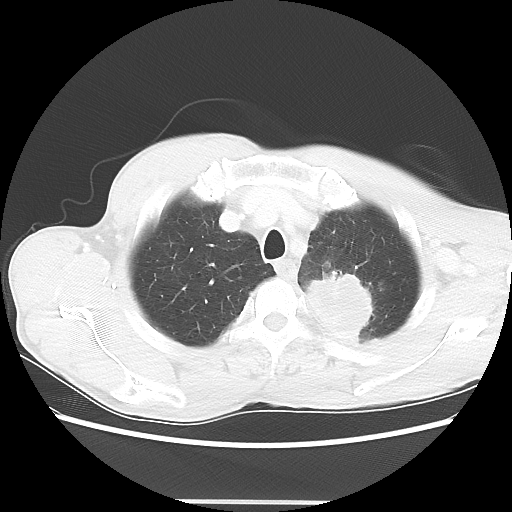
Chest CT, one axial slice. Reconstruction kernel LUNG. 100 kVp. Lung window (W 1500 / L -600 HU). 5 mm slice thickness. 512 × 512 image matrix, field of view 360 × 360 mm. Male patient, age 61 years. From the clinical record (not read from this slice): clinical TNM (as recorded): T3 N1 M1.
Outlined on this slice (rectangle marked by the reading radiologist):
- lung tumour (recorded histology: adenocarcinoma): box from (x=299, y=270) to (x=378, y=354) px